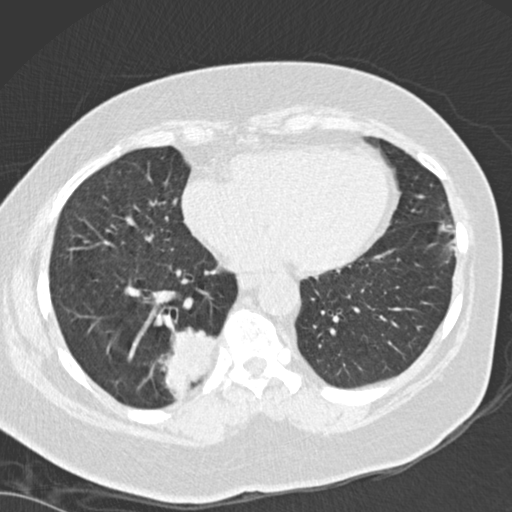
Low-dose screening chest CT, axial slice, baseline screening round, lung window (W 1500 / L -600 HU), 2 mm slice thickness, slice 104 of 162 in the series. Female participant, aged 66 years at enrolment.
Lesion marked by an expert reader, box from (x=146, y=316) to (x=232, y=405) px. The screening reader recorded 3 non-calcified nodules or masses ≥4 mm on this exam (left lower lobe, left lower lobe, right lower lobe); which of them this box marks is not recorded. Official screen result: positive, change unspecified: nodule(s) >= 4 mm or enlarging nodule(s), mass(es), or other non-specific abnormalities suspicious for lung cancer. Later outcome: lung cancer diagnosed 67 days after this screen — adenocarcinoma, NOS, right lower lobe, well differentiated (G1), stage IB (AJCC 6th edition), 55 mm at pathology.